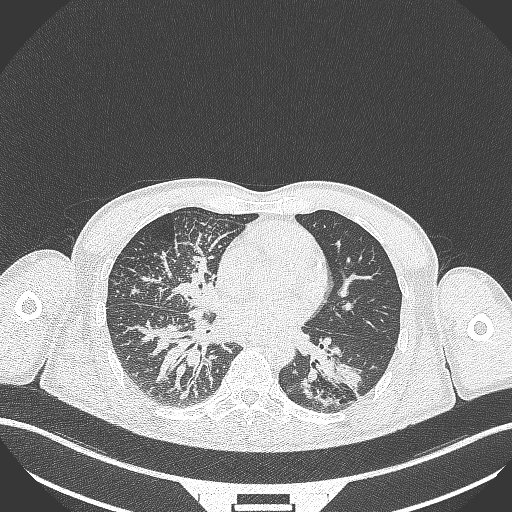
Chest CT, one axial slice. Position 144 of 348 along the scan axis. Reconstruction kernel B70f. 120 kVp. Lung window (W 1500 / L -600 HU). 1 mm slice thickness. 512 × 512 image matrix. Patient: male, 49 years. From the clinical record (not read from this slice): clinical TNM (as recorded): T2b N1 M0.
Structures marked on this image (bounding box drawn by a radiologist):
- lung tumour (recorded histology: adenocarcinoma): bounding box [x1, y1, x2, y2] px = [298, 352, 364, 408]